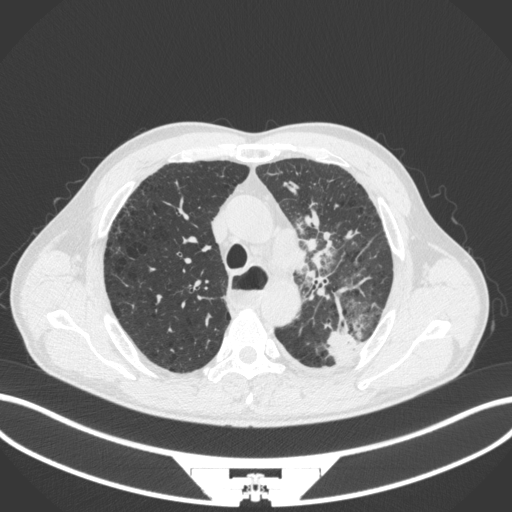
Chest CT, one axial slice. Position 284 of 411 along the scan axis. Reconstruction kernel B31f. 120 kVp. Lung window (W 1500 / L -600 HU). 512 × 512 image matrix, field of view 400 × 400 mm. Male patient, age 57 years. From the clinical record (not read from this slice): clinical TNM (as recorded): T2a N1 M0.
Outlined on this slice (rectangle marked by the reading radiologist):
- lung tumour (recorded histology: squamous cell carcinoma): bounding box [x1, y1, x2, y2] px = [285, 229, 320, 282]